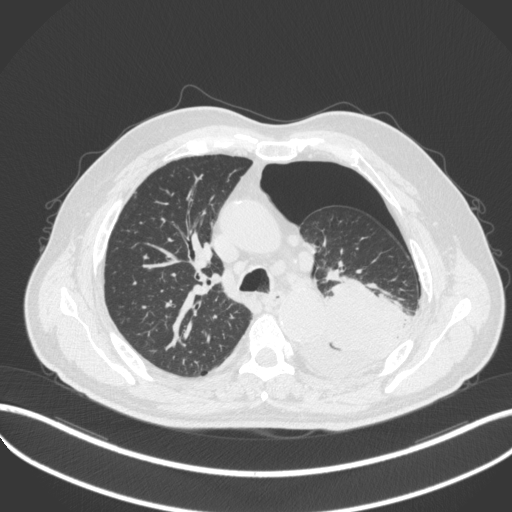
Chest CT, one axial slice. Reconstruction kernel B31f. 120 kVp. Lung window (W 1500 / L -600 HU). 1 mm slice thickness. 512 × 512 image matrix, field of view 400 × 400 mm. Patient: male, 76 years. From the clinical record (not read from this slice): clinical TNM (as recorded): T3 N0 M1b.
Annotated regions visible in this slice (rectangle marked by the reading radiologist):
- lung tumour (recorded histology: adenocarcinoma): bounding box (x1, y1, x2, y2) in pixels: (304, 281, 412, 380)